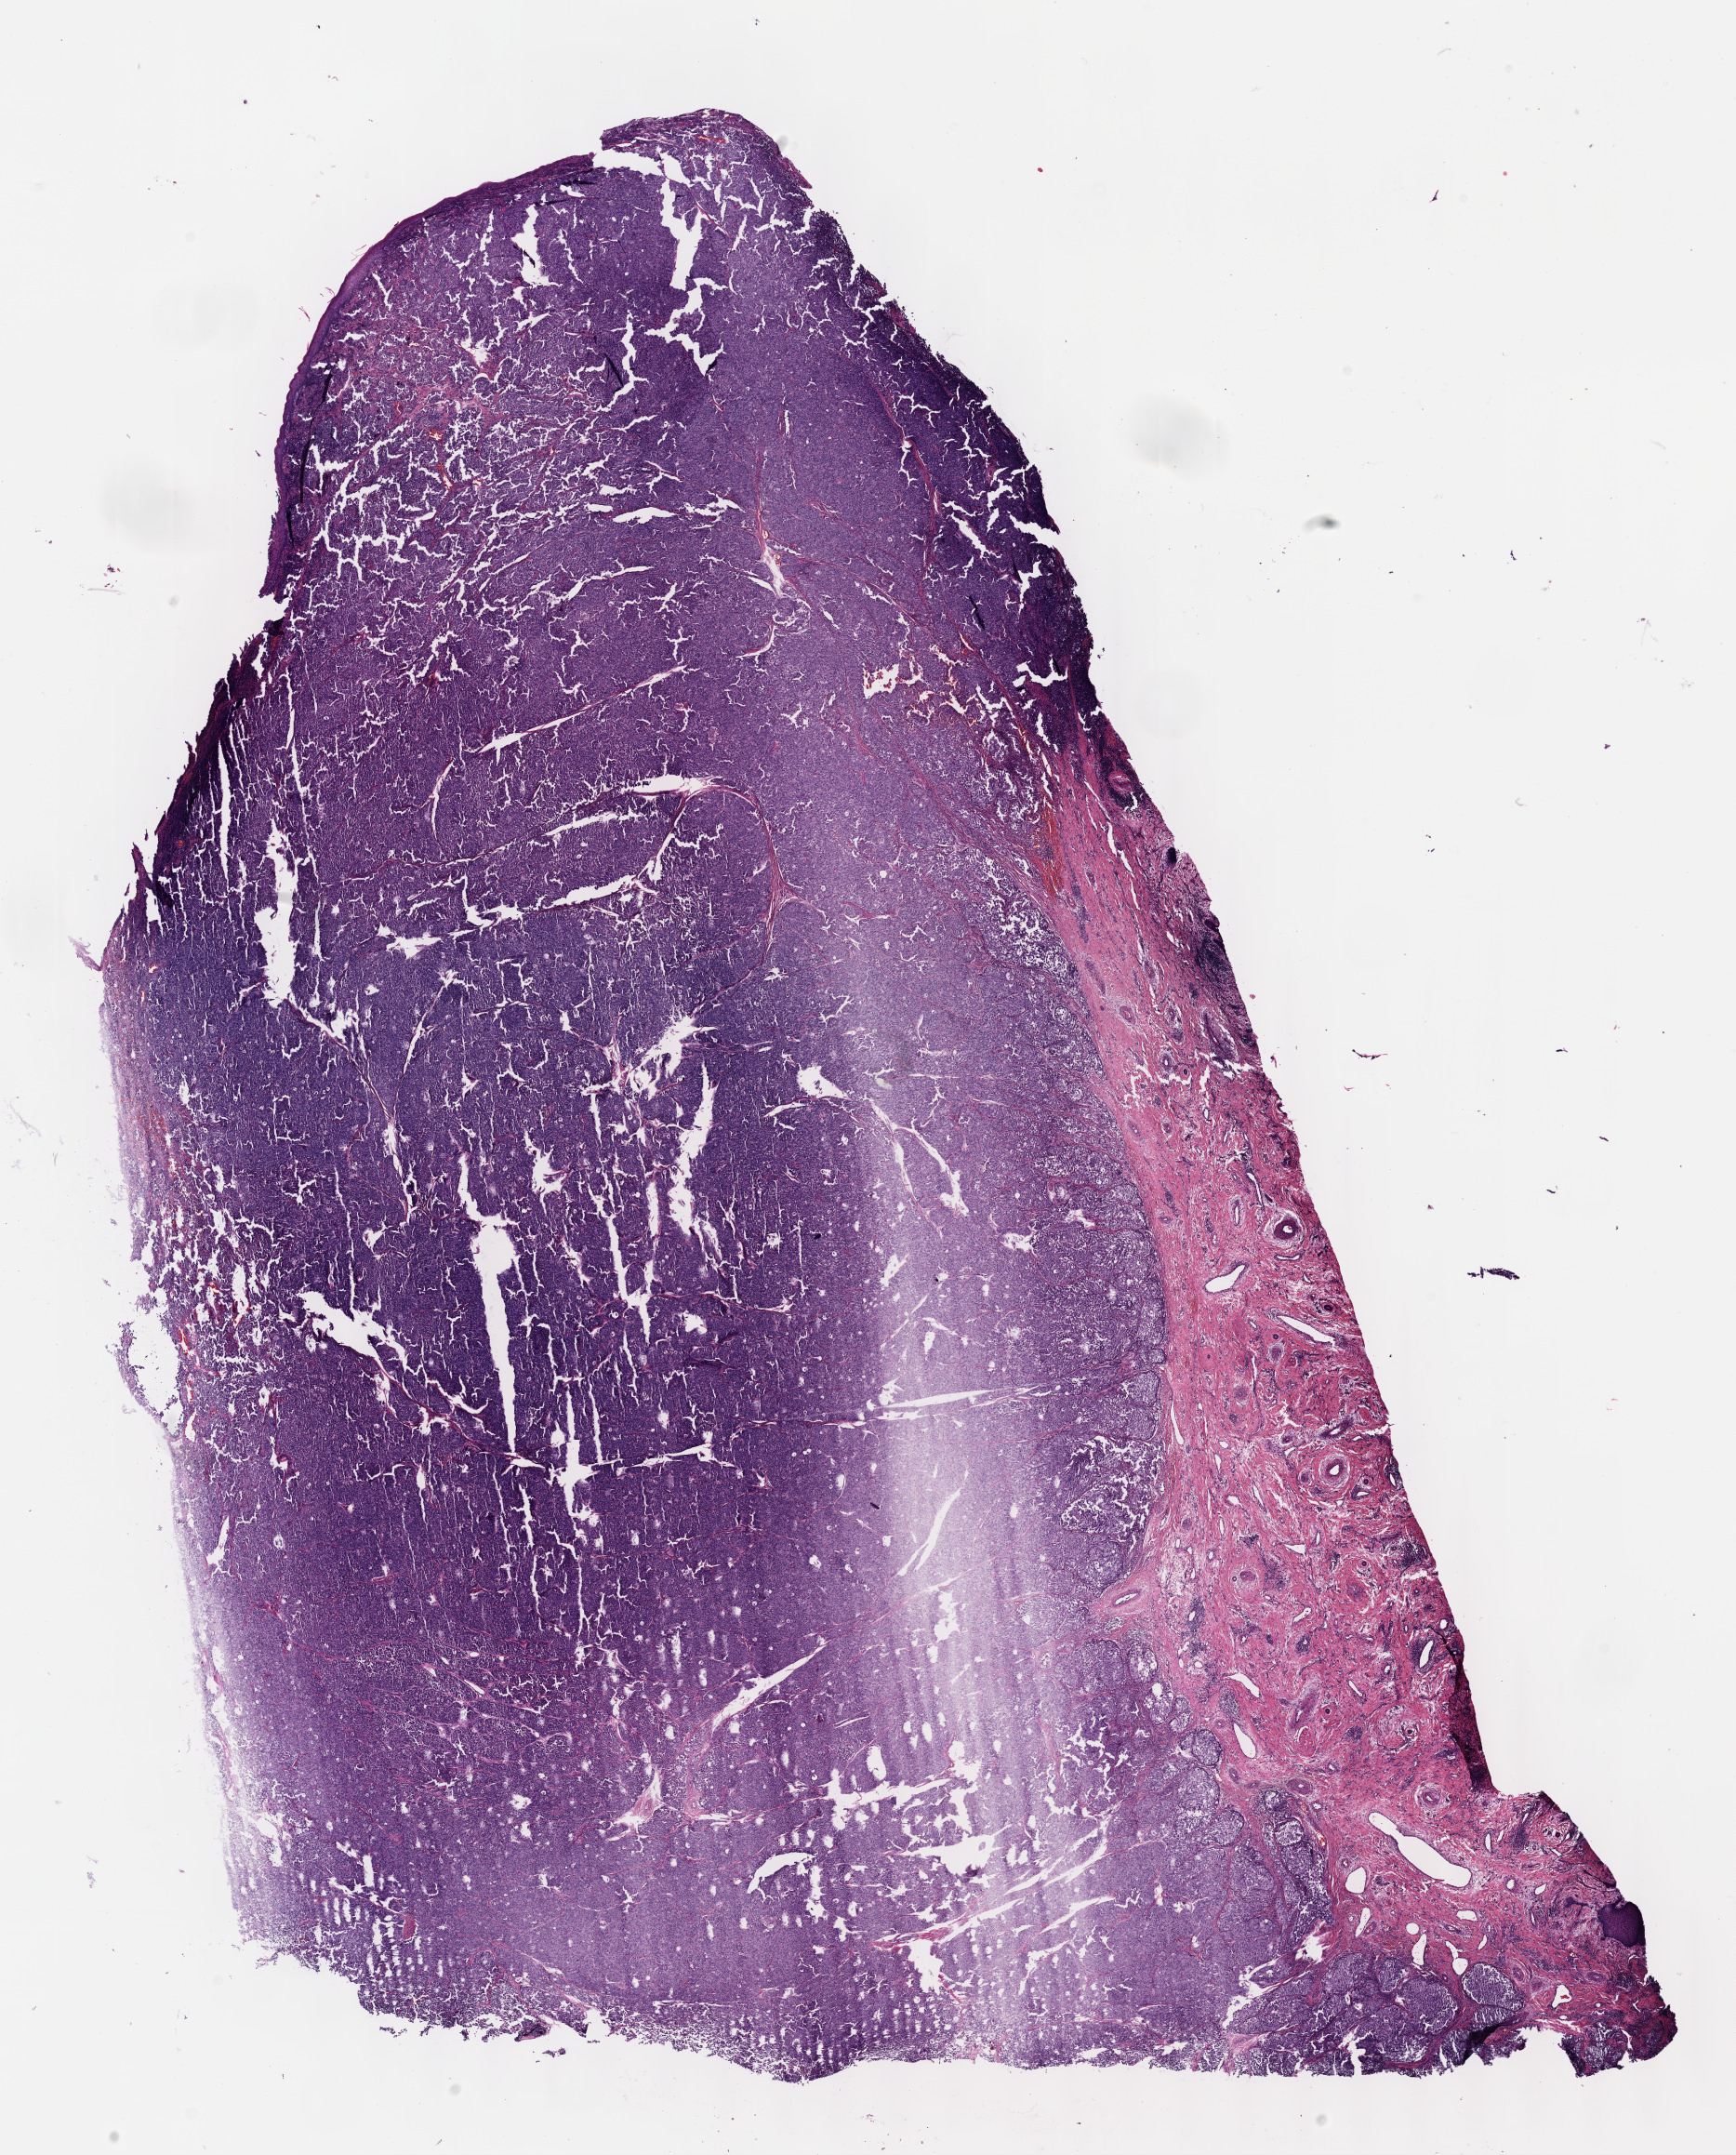
H&E whole-slide image, whole scanned area (about 15.1 x 18.7 mm, from a 40x scan) shown as a low-resolution overview. FFPE section. Primary tumour sample from the skin. Male, age 86 years at initial diagnosis.
AJCC pathologic stage: IIC. Histologic diagnosis: Epithelioid cell melanoma.